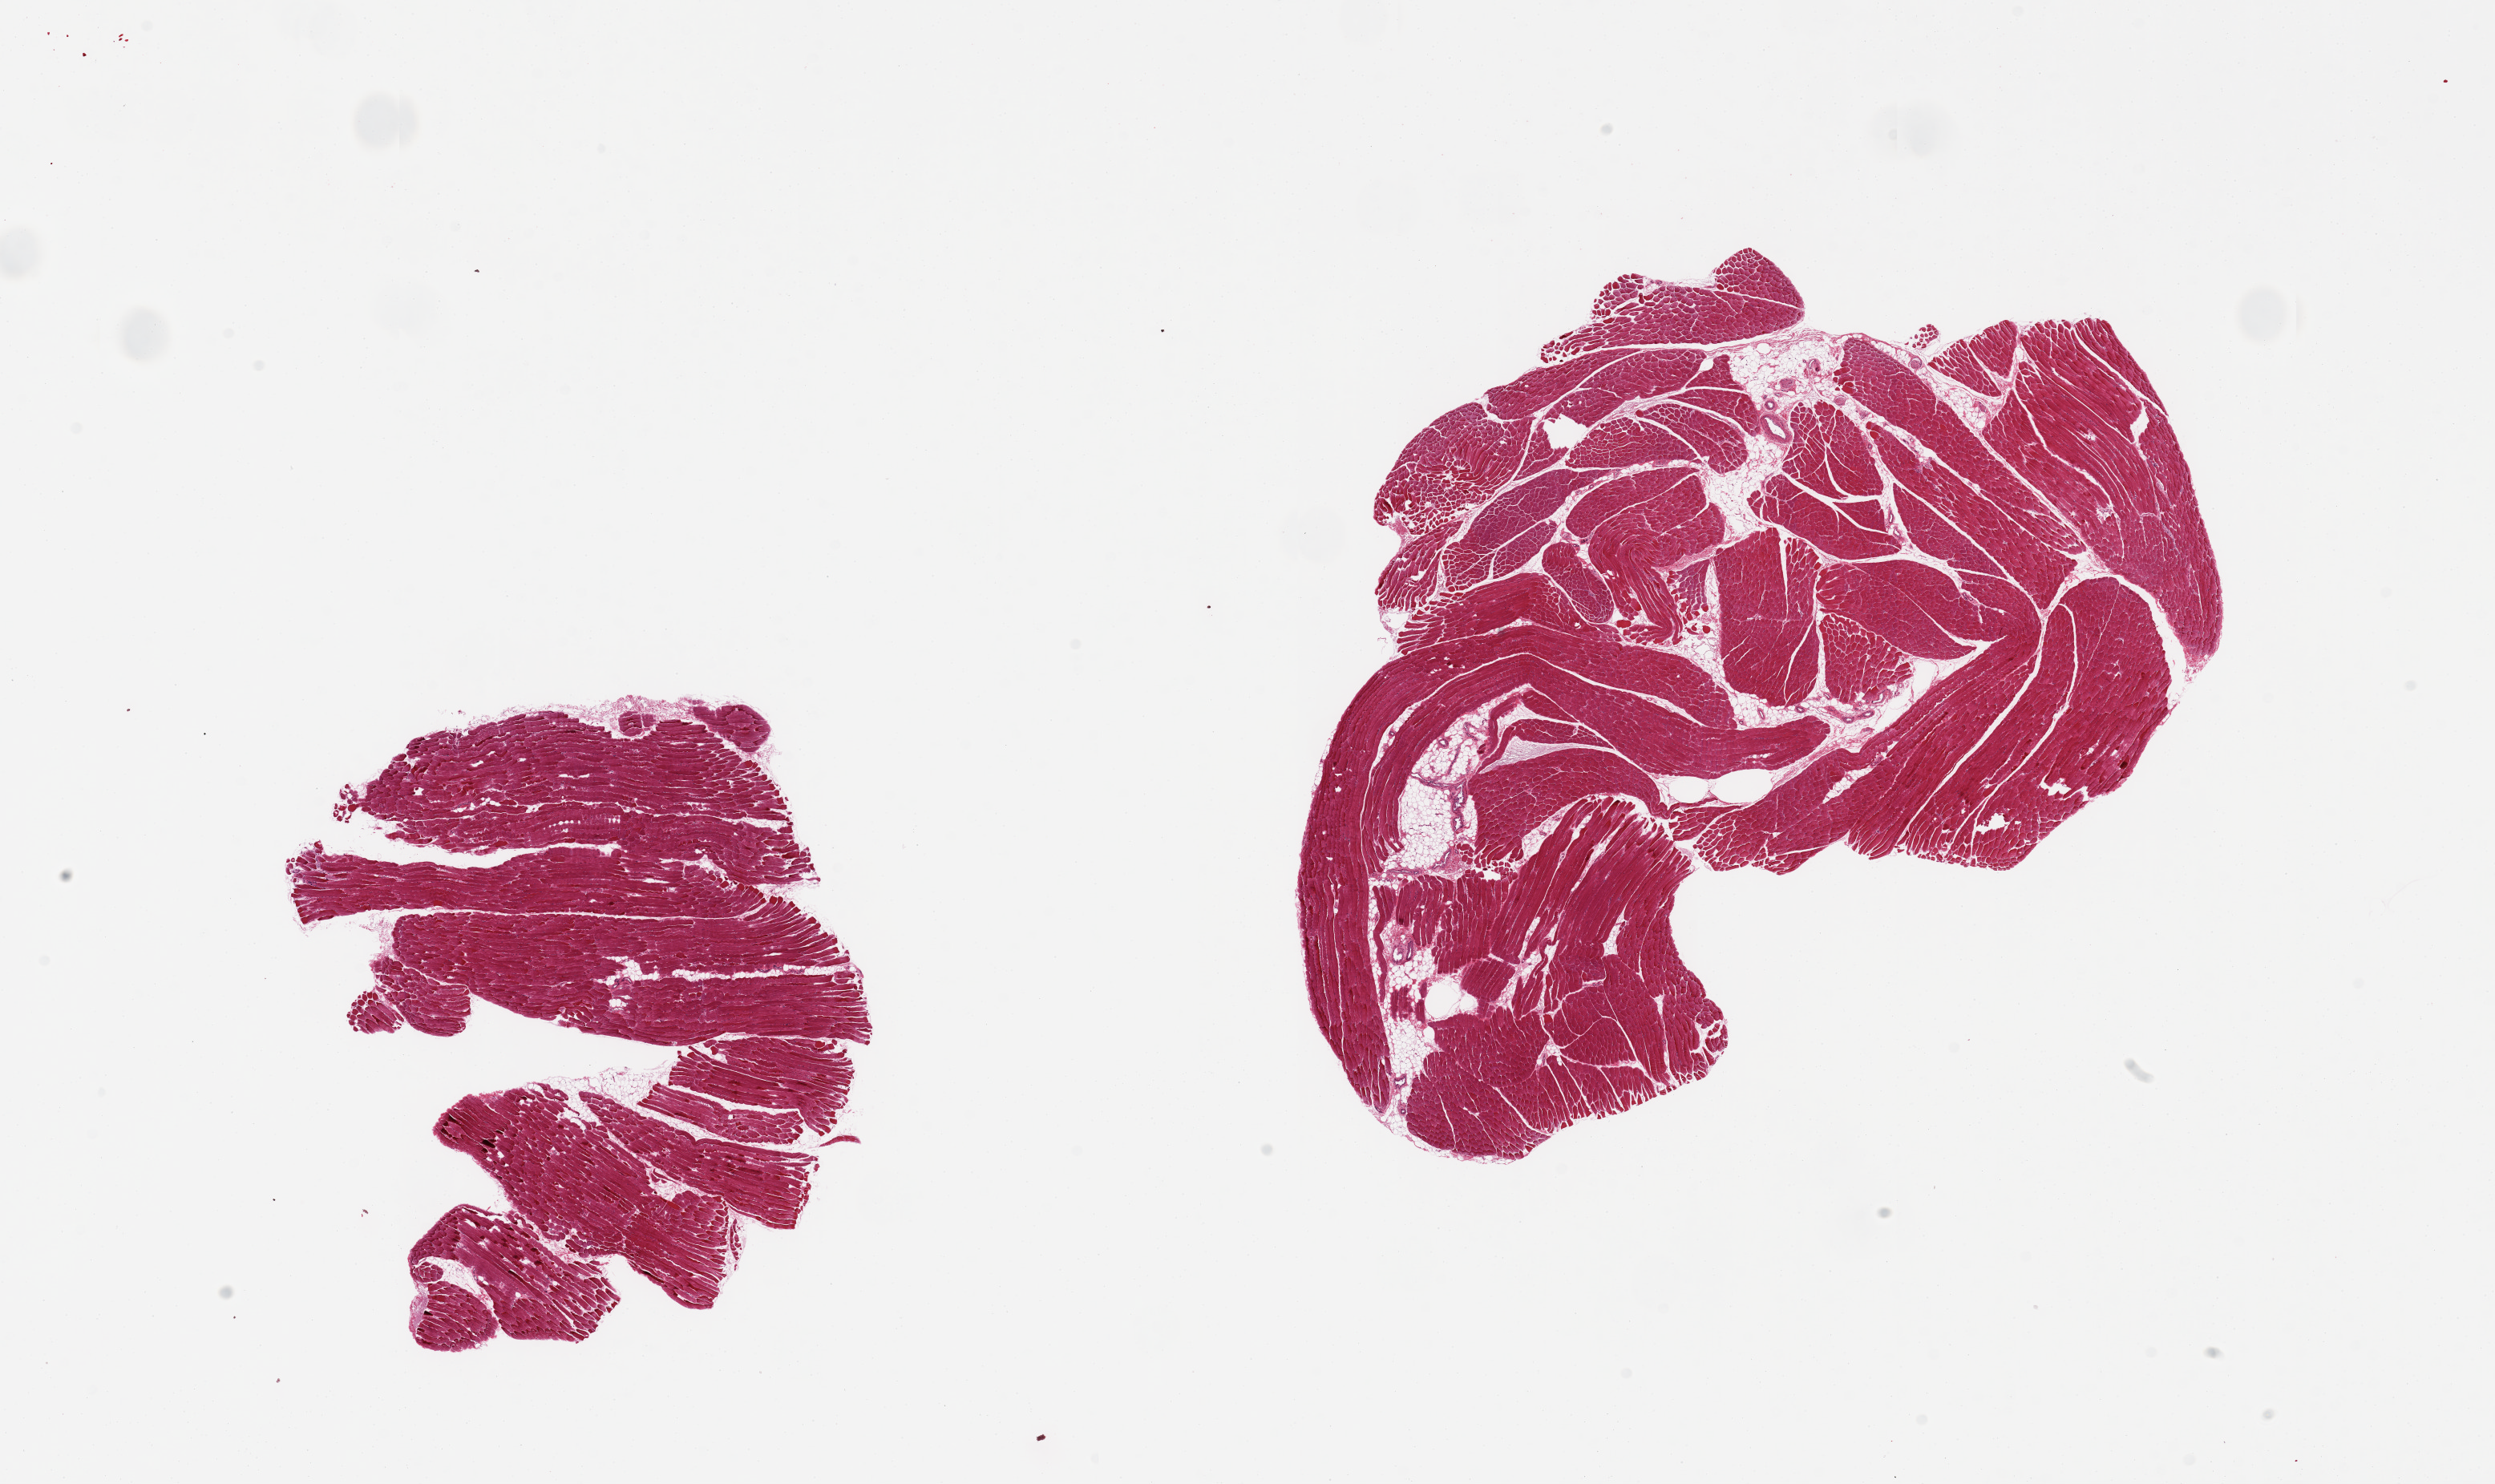
H&E whole-slide image, a low-resolution overview of the entire scanned area, about 24.6 x 14.6 mm. PAXgene-fixed, paraffin-embedded tissue. Sampled site (target tissue): skeletal muscle. Donor tissue sample. Donor: male.
Pathologist's review note for this sample: 2 pieces, includes 5-10% internal adipose tissue.